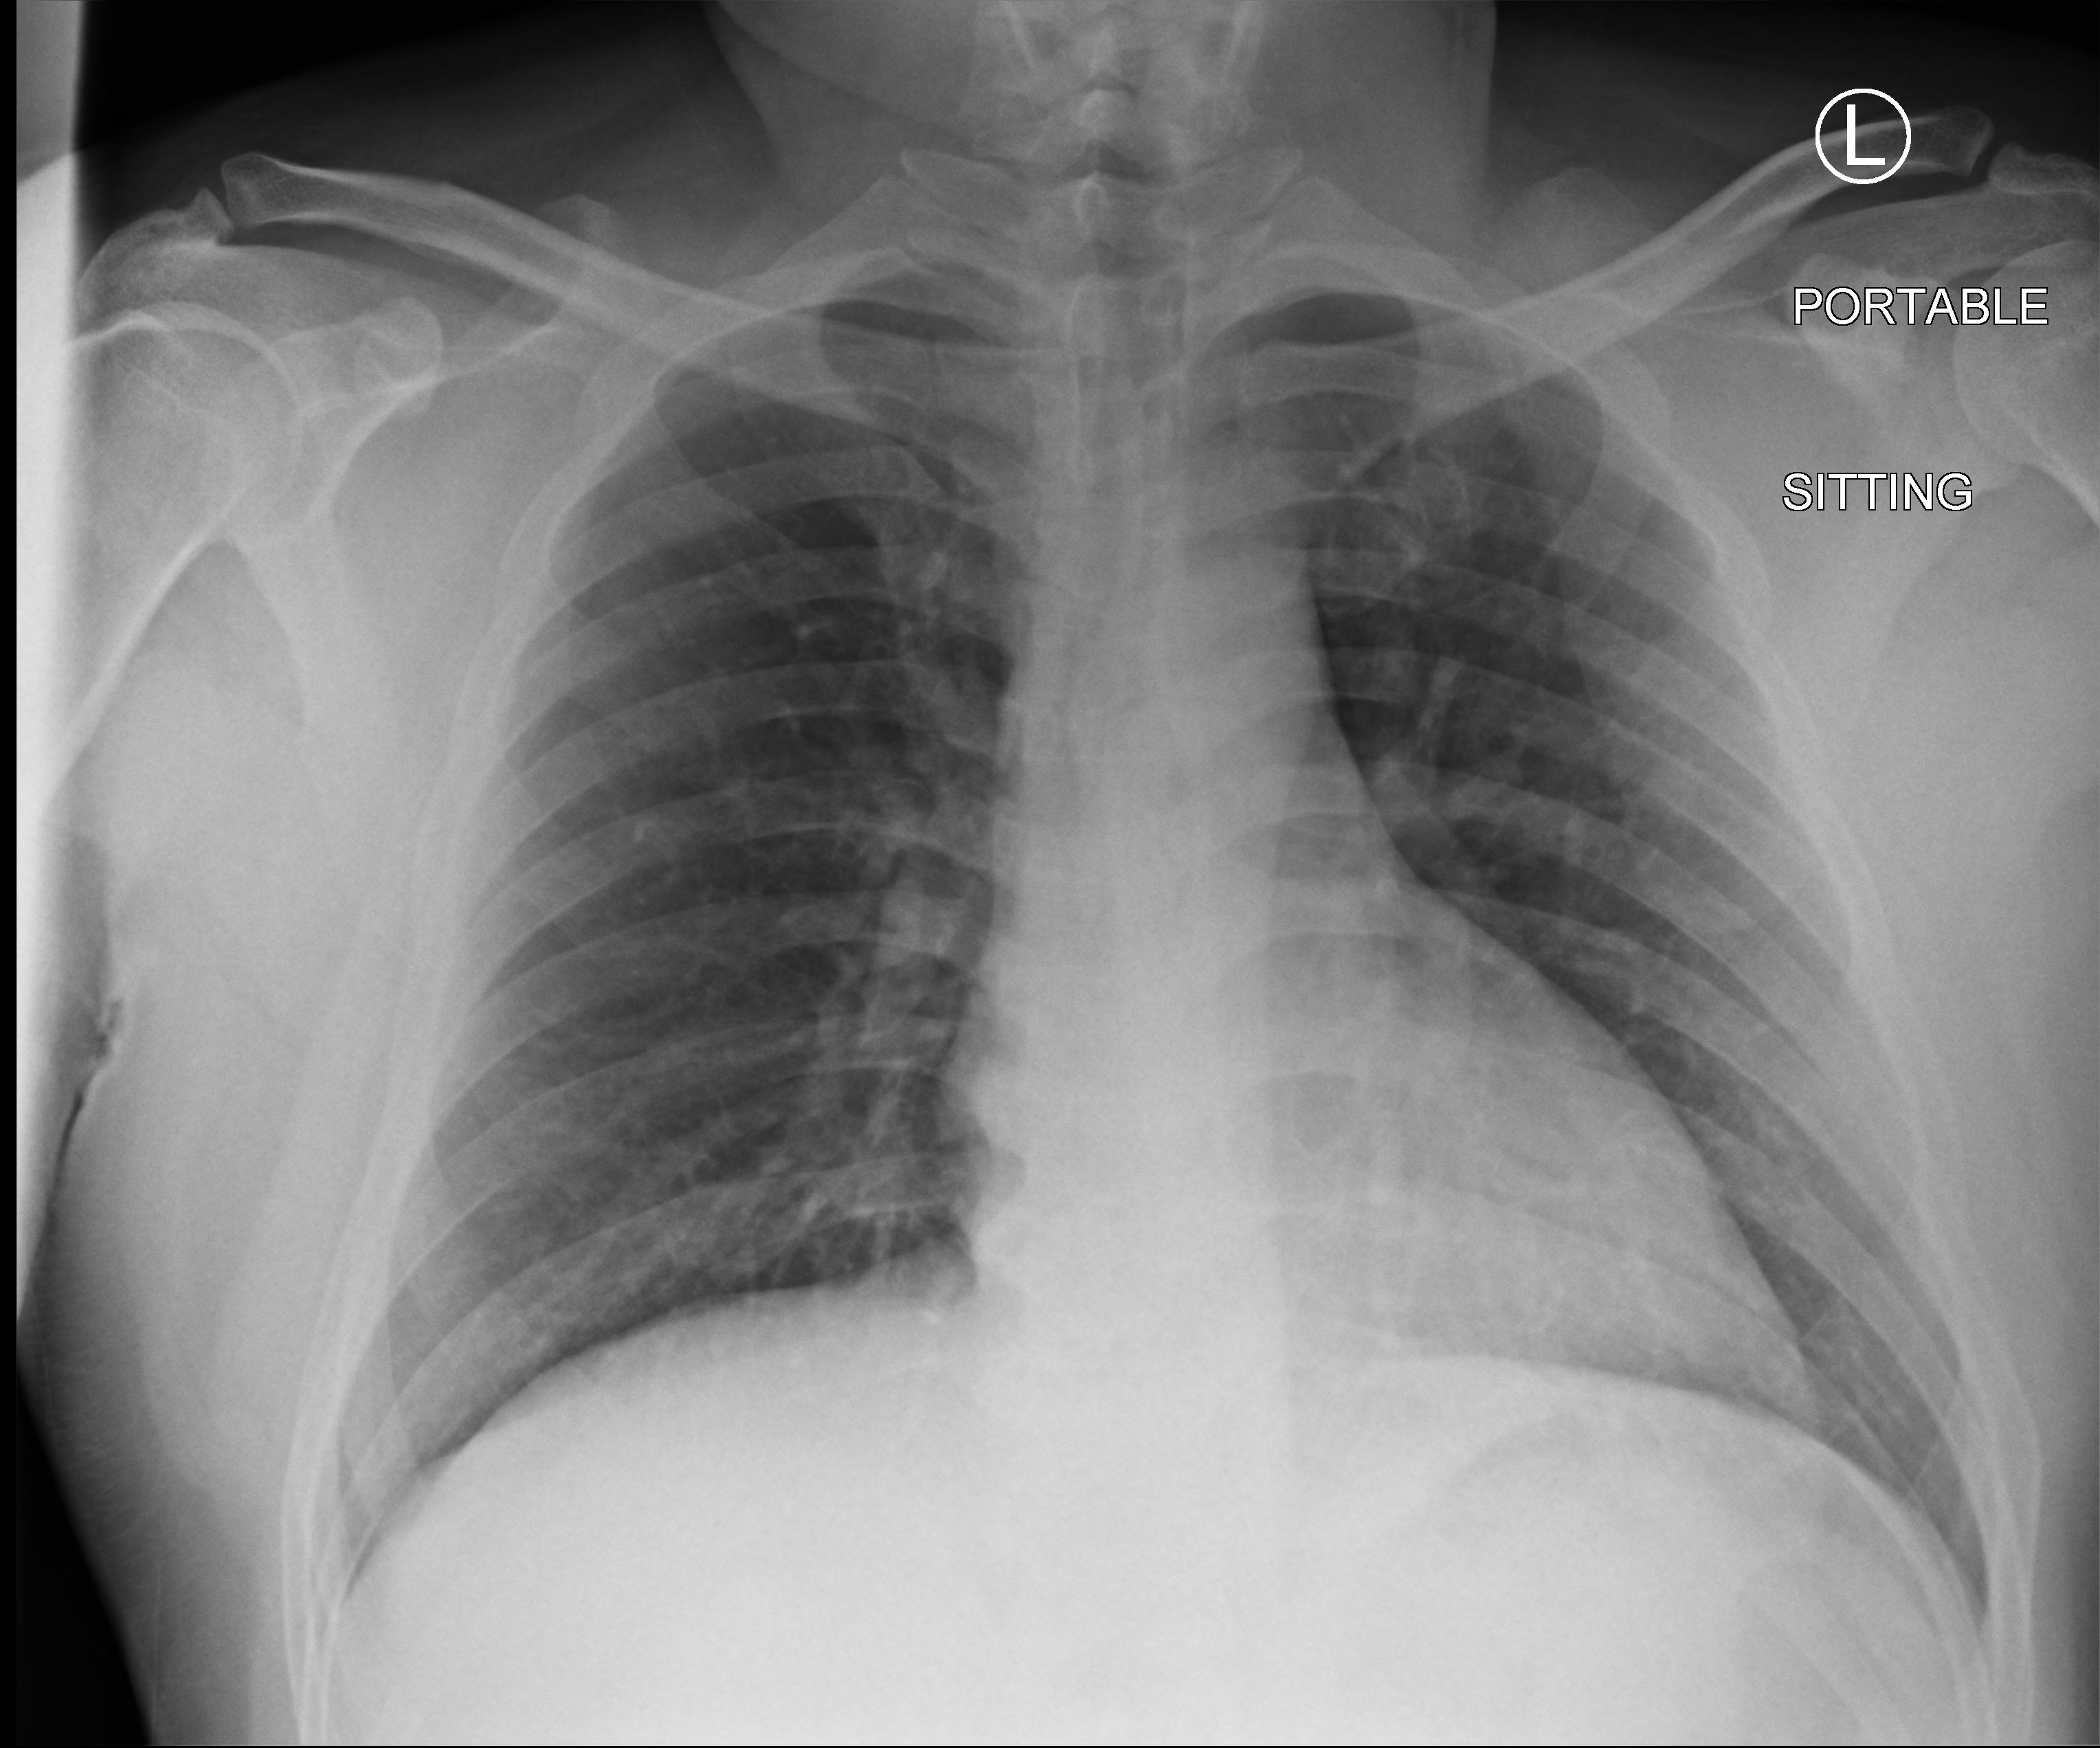
Bedside chest radiograph (computed radiography); anteroposterior (AP) projection. Patient hospitalised with COVID-19; male, aged 18–59 years.
Admission-level facts for this patient (not findings on this image; timing relative to this image not recorded): mechanically ventilated during this hospital stay: no; smoking status (admission record): never.